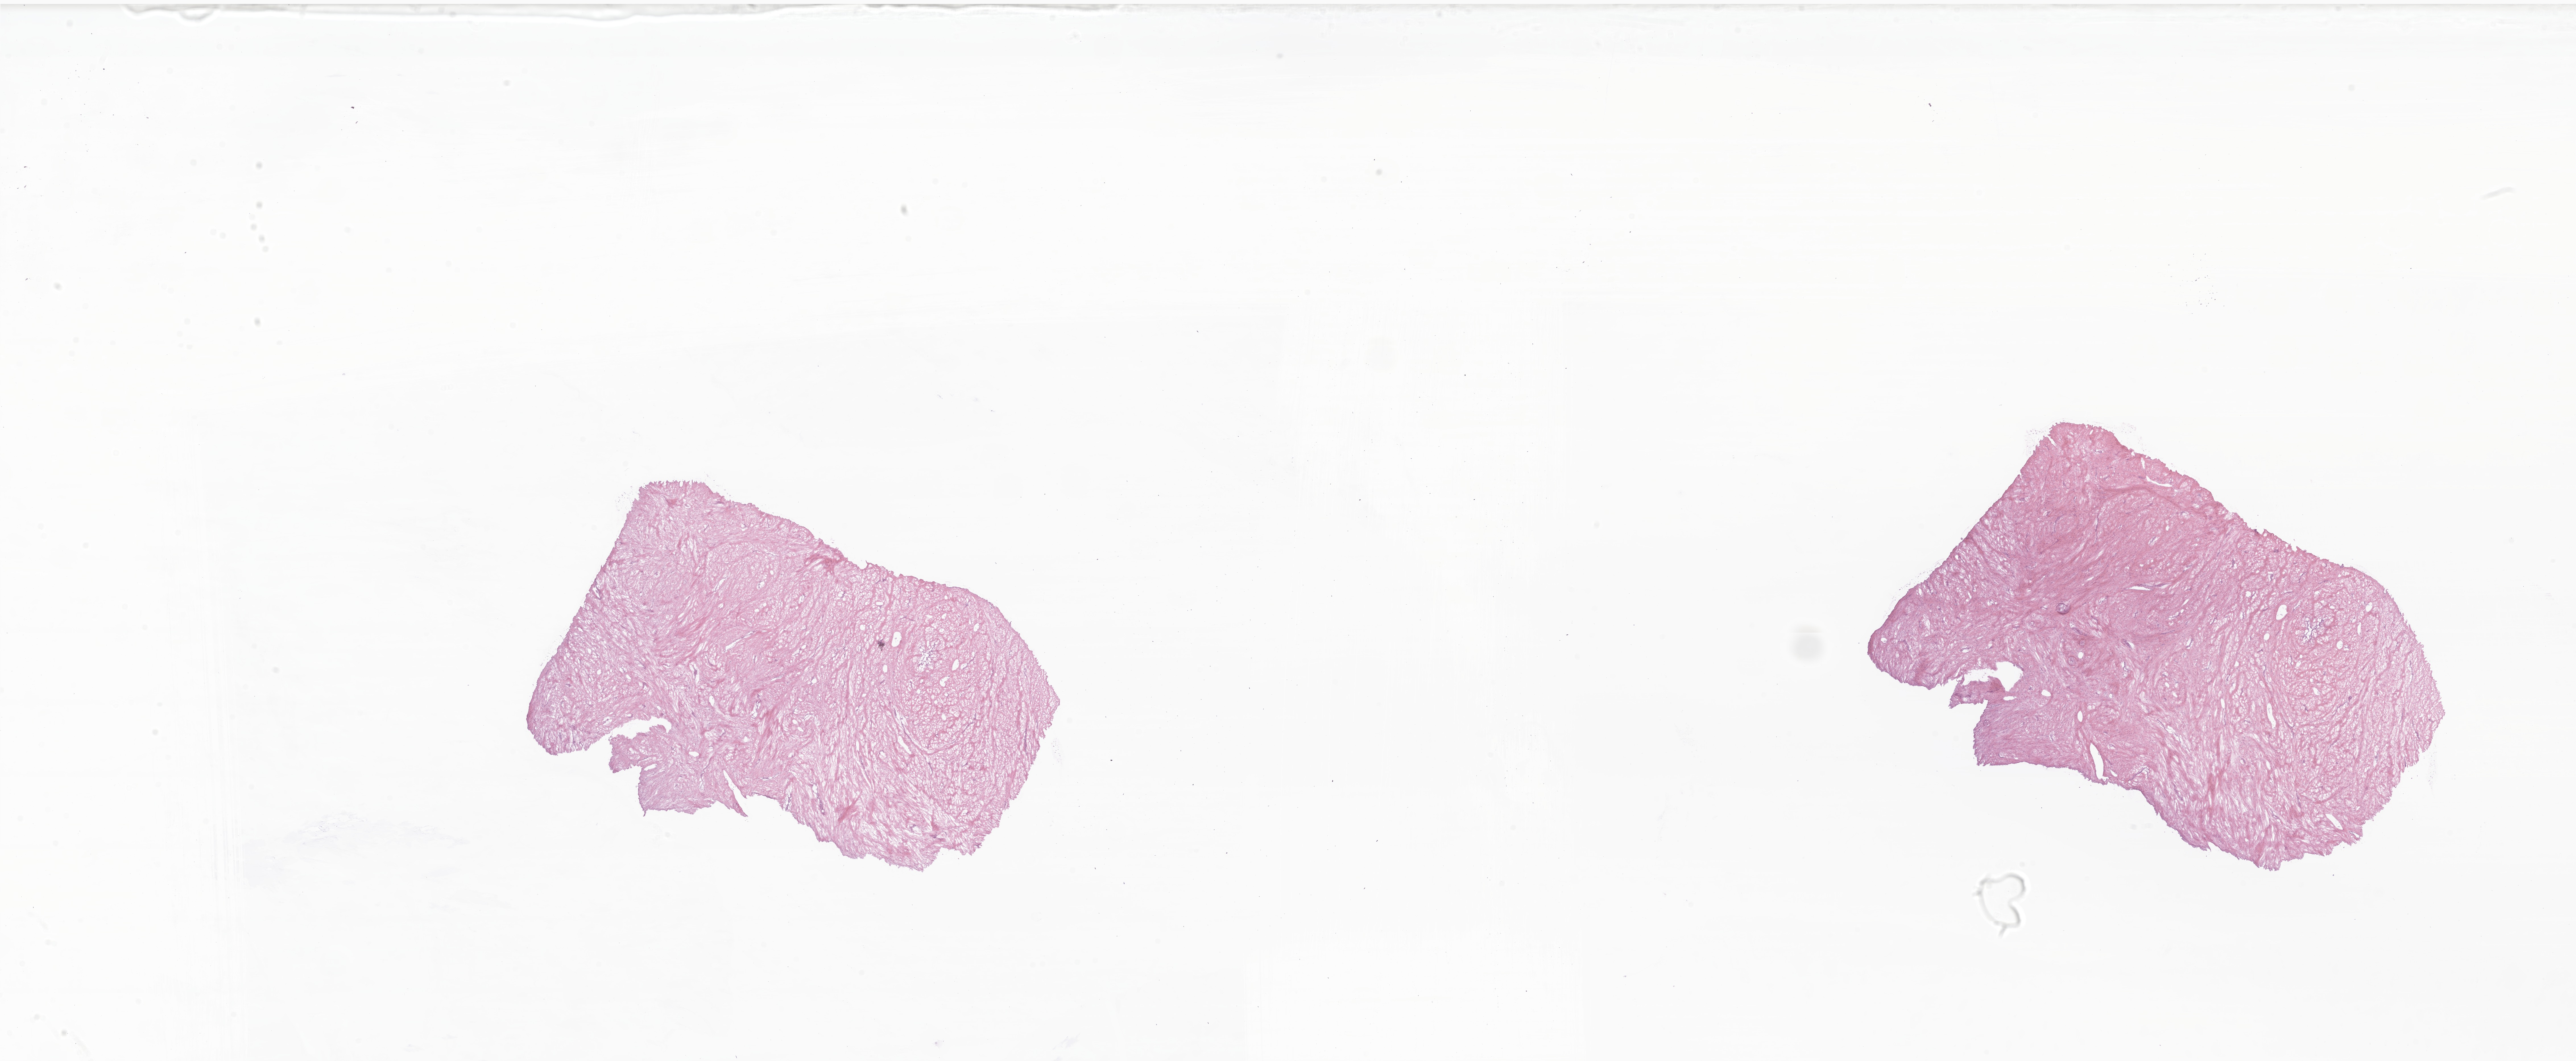
Digitized hematoxylin and eosin (H&E)-stained section of tumor tissue from the head and neck — low-resolution overview of the scanned area, about 38.2 x 15.7 mm, frozen section. Patient: female, age 78 months (6 years 6 months).
Diagnosis (ICD-O-3 morphology term): Myxofibrosarcoma. Tissue or organ of origin (case record): head, face or neck.